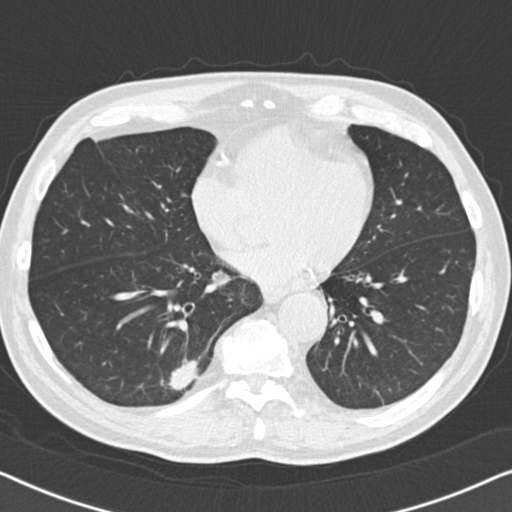
Low-dose screening chest CT, one axial slice; position 54 of 164 along the scan axis; lung window (W 1500 / L -600 HU); 2 mm slice thickness; 512 × 512 image matrix.
Outlined on this slice (manually delineated by an expert):
- lesion 1 (tumor, lower lobe of right lung): bounding box [x1, y1, x2, y2] px = [169, 359, 198, 391]